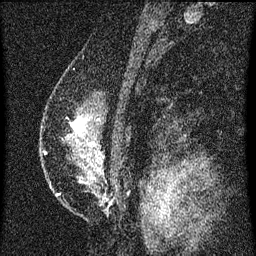
Breast MRI (dynamic contrast-enhanced), one sagittal slice; slice 40 of 60 in the series (ordered by position); dynamic contrast-enhanced series, image 2 of 3 at this slice position (ordered by acquisition); 1.5 T; TE 4.2 ms, TR 8 ms; 256 × 256 image matrix, field of view 180 × 180 mm. Female patient, age 47 years.
Annotated regions visible in this slice (semi-automatically segmented with operator editing):
- analysis volume of interest (the breast-tissue region the enhancement analysis was run in; not a lesion): bounding box [x1, y1, x2, y2] px = [54, 84, 128, 203]
- tumour enhancement mask (voxels above the 70 % enhancement threshold inside the analysis volume of interest): [72, 118, 84, 133]